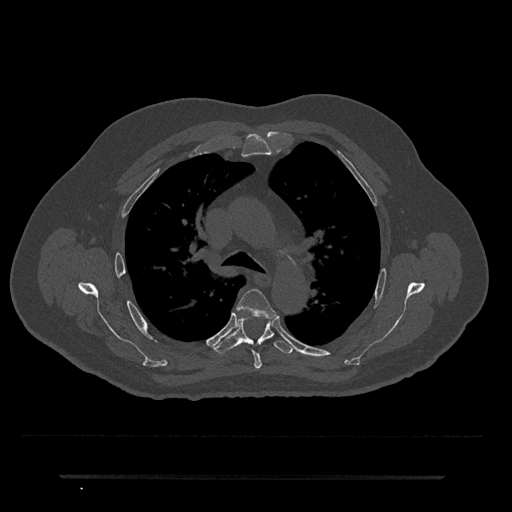
CT including the spine, one axial slice; position 503 of 797 along the scan axis; reconstruction kernel Br40s/3; 120 kVp; bone window (W 1800 / L 400 HU); 0.5 mm slice thickness; 512 × 512 image matrix, field of view 437 × 437 mm. Patient: male, 69 years. Case-level facts recorded for this patient, not image findings: primary cancer: prostate.
Annotated regions visible in this slice (semi-automatically segmented with operator editing):
- T4 vertebra: bounding box [x1, y1, x2, y2] px = [237, 289, 277, 369]
- T5 vertebra: [212, 317, 294, 354]